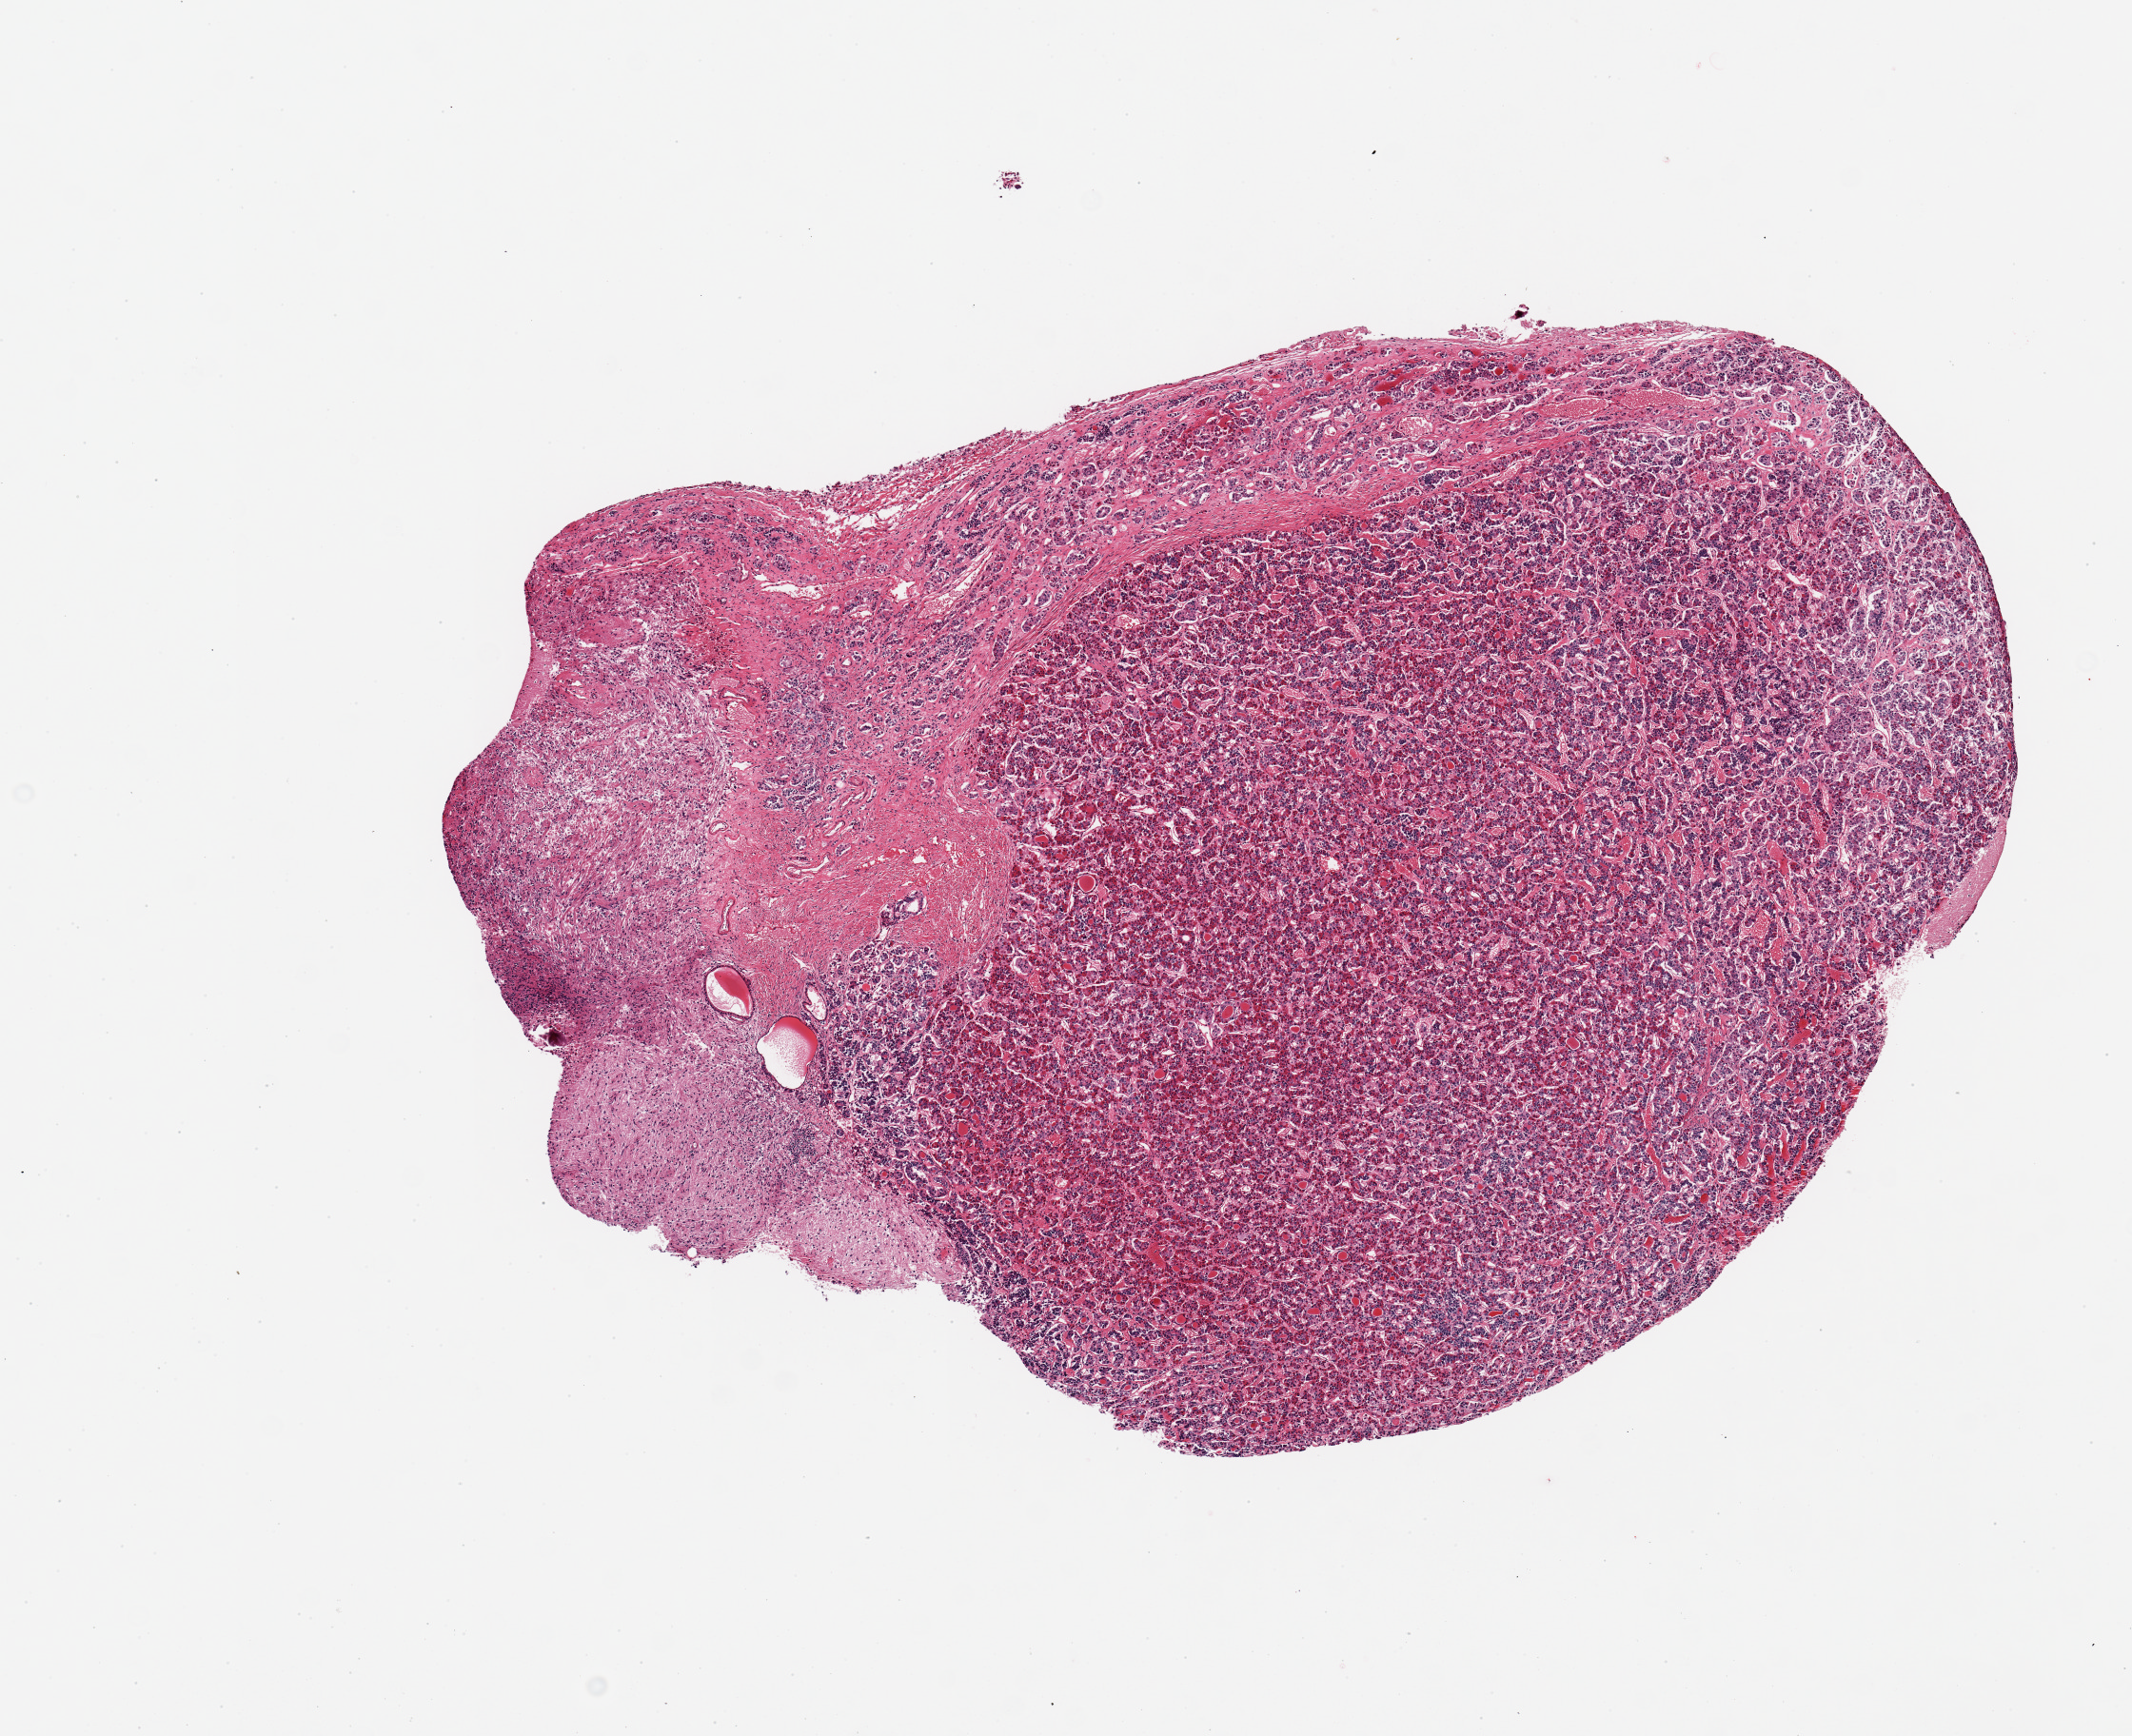
Digitized hematoxylin and eosin (H&E)-stained section — whole scanned area (about 8.9 x 7.2 mm, acquisition: 20x scan) shown as a low-resolution overview, PAXgene-fixed, paraffin-embedded tissue, target tissue: pituitary, tissue donor sample.
Review note (as recorded): 1 piece; mostly anterior.